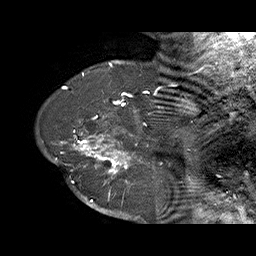
Breast MRI (dynamic contrast-enhanced), one sagittal slice. Slice 56 of 70 in the series (ordered by position). Dynamic contrast-enhanced series, time point 2 of 6 at this slice position (early post-contrast). 1.5 T. TE 4.5 ms, TR 32.4 ms. 3 mm slice thickness. 256 × 256 image matrix, field of view 180 × 180 mm. Female patient. Case-level facts recorded for this patient, not image findings: setting: breast cancer imaged before/during neoadjuvant chemotherapy; receptor status: HR-positive, HER2-negative.
Structures marked on this image (semi-automatically segmented with operator editing):
- analysis volume of interest (the breast-tissue region the enhancement analysis was run in; not a lesion): bounding box <71,128,159,202> (left, top, right, bottom; pixels)
- tumour enhancement mask (voxels above the 100 % enhancement threshold inside the analysis volume of interest): <71,129,149,202>